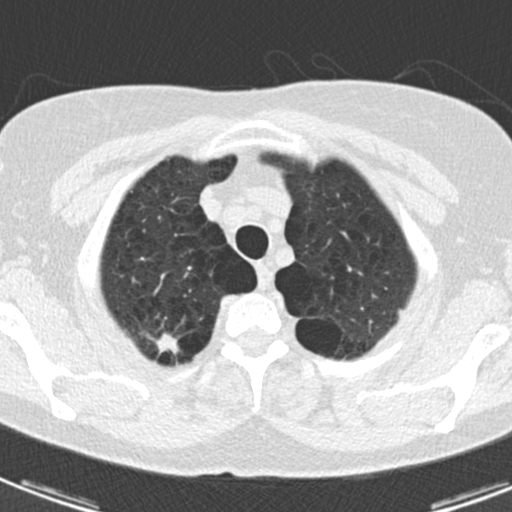
Chest CT (low-dose screening protocol), one axial image. Third screening round (two years after baseline). Lung window (W 1500 / L -600 HU). 120 kVp. Slice 21 of 174 in the series. Female, age 59 years at enrolment. Current smoker at enrolment.
Expert reader's lesion annotation, box from (x=131, y=320) to (x=188, y=365) px. Screening reader's record for this exam (one nodule recorded; not confirmed to be the boxed lesion): non-calcified nodule or mass ≥4 mm, right upper lobe, 12 × 7 mm, spiculated (stellate) margins, soft tissue attenuation, pre-existing on the prior screen: yes; interval growth: yes. Participant outcome: lung cancer diagnosed 32 days after this screen — adenocarcinoma, NOS, right upper lobe, poorly differentiated (G3), stage IA (AJCC 6th edition), 20 mm at pathology.